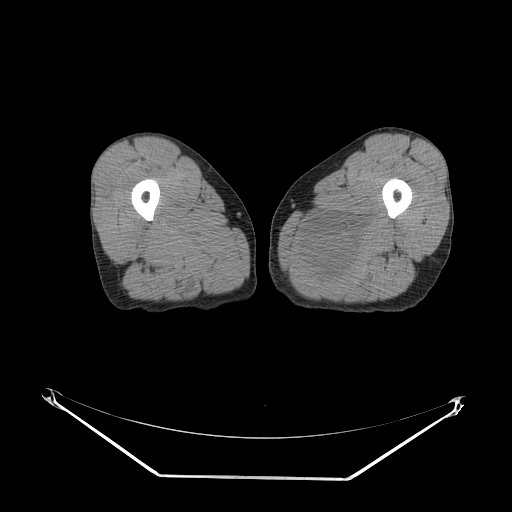
CT of an extremity soft-tissue mass (from a PET/CT study), one axial slice. Slice 16 of 267 in the series (ordered by position). Reconstruction kernel SOFT. 140 kVp. Soft-tissue window (W 400 / L 40 HU). 3.75 mm slice thickness. 512 × 512 image matrix, field of view 500 × 500 mm. Male patient. Case-level facts recorded for this patient, not image findings: histological type: pleiomorphic liposarcoma; grade: high; site of the primary tumour: left thigh.
Structures marked on this image (expert contour drawn on MRI and transferred to this co-registered scan by the dataset authors):
- gross tumour volume including surrounding oedema: bounding box (x1, y1, x2, y2) in pixels: (304, 206, 378, 286)
- gross tumour volume (mass): (310, 237, 360, 282)